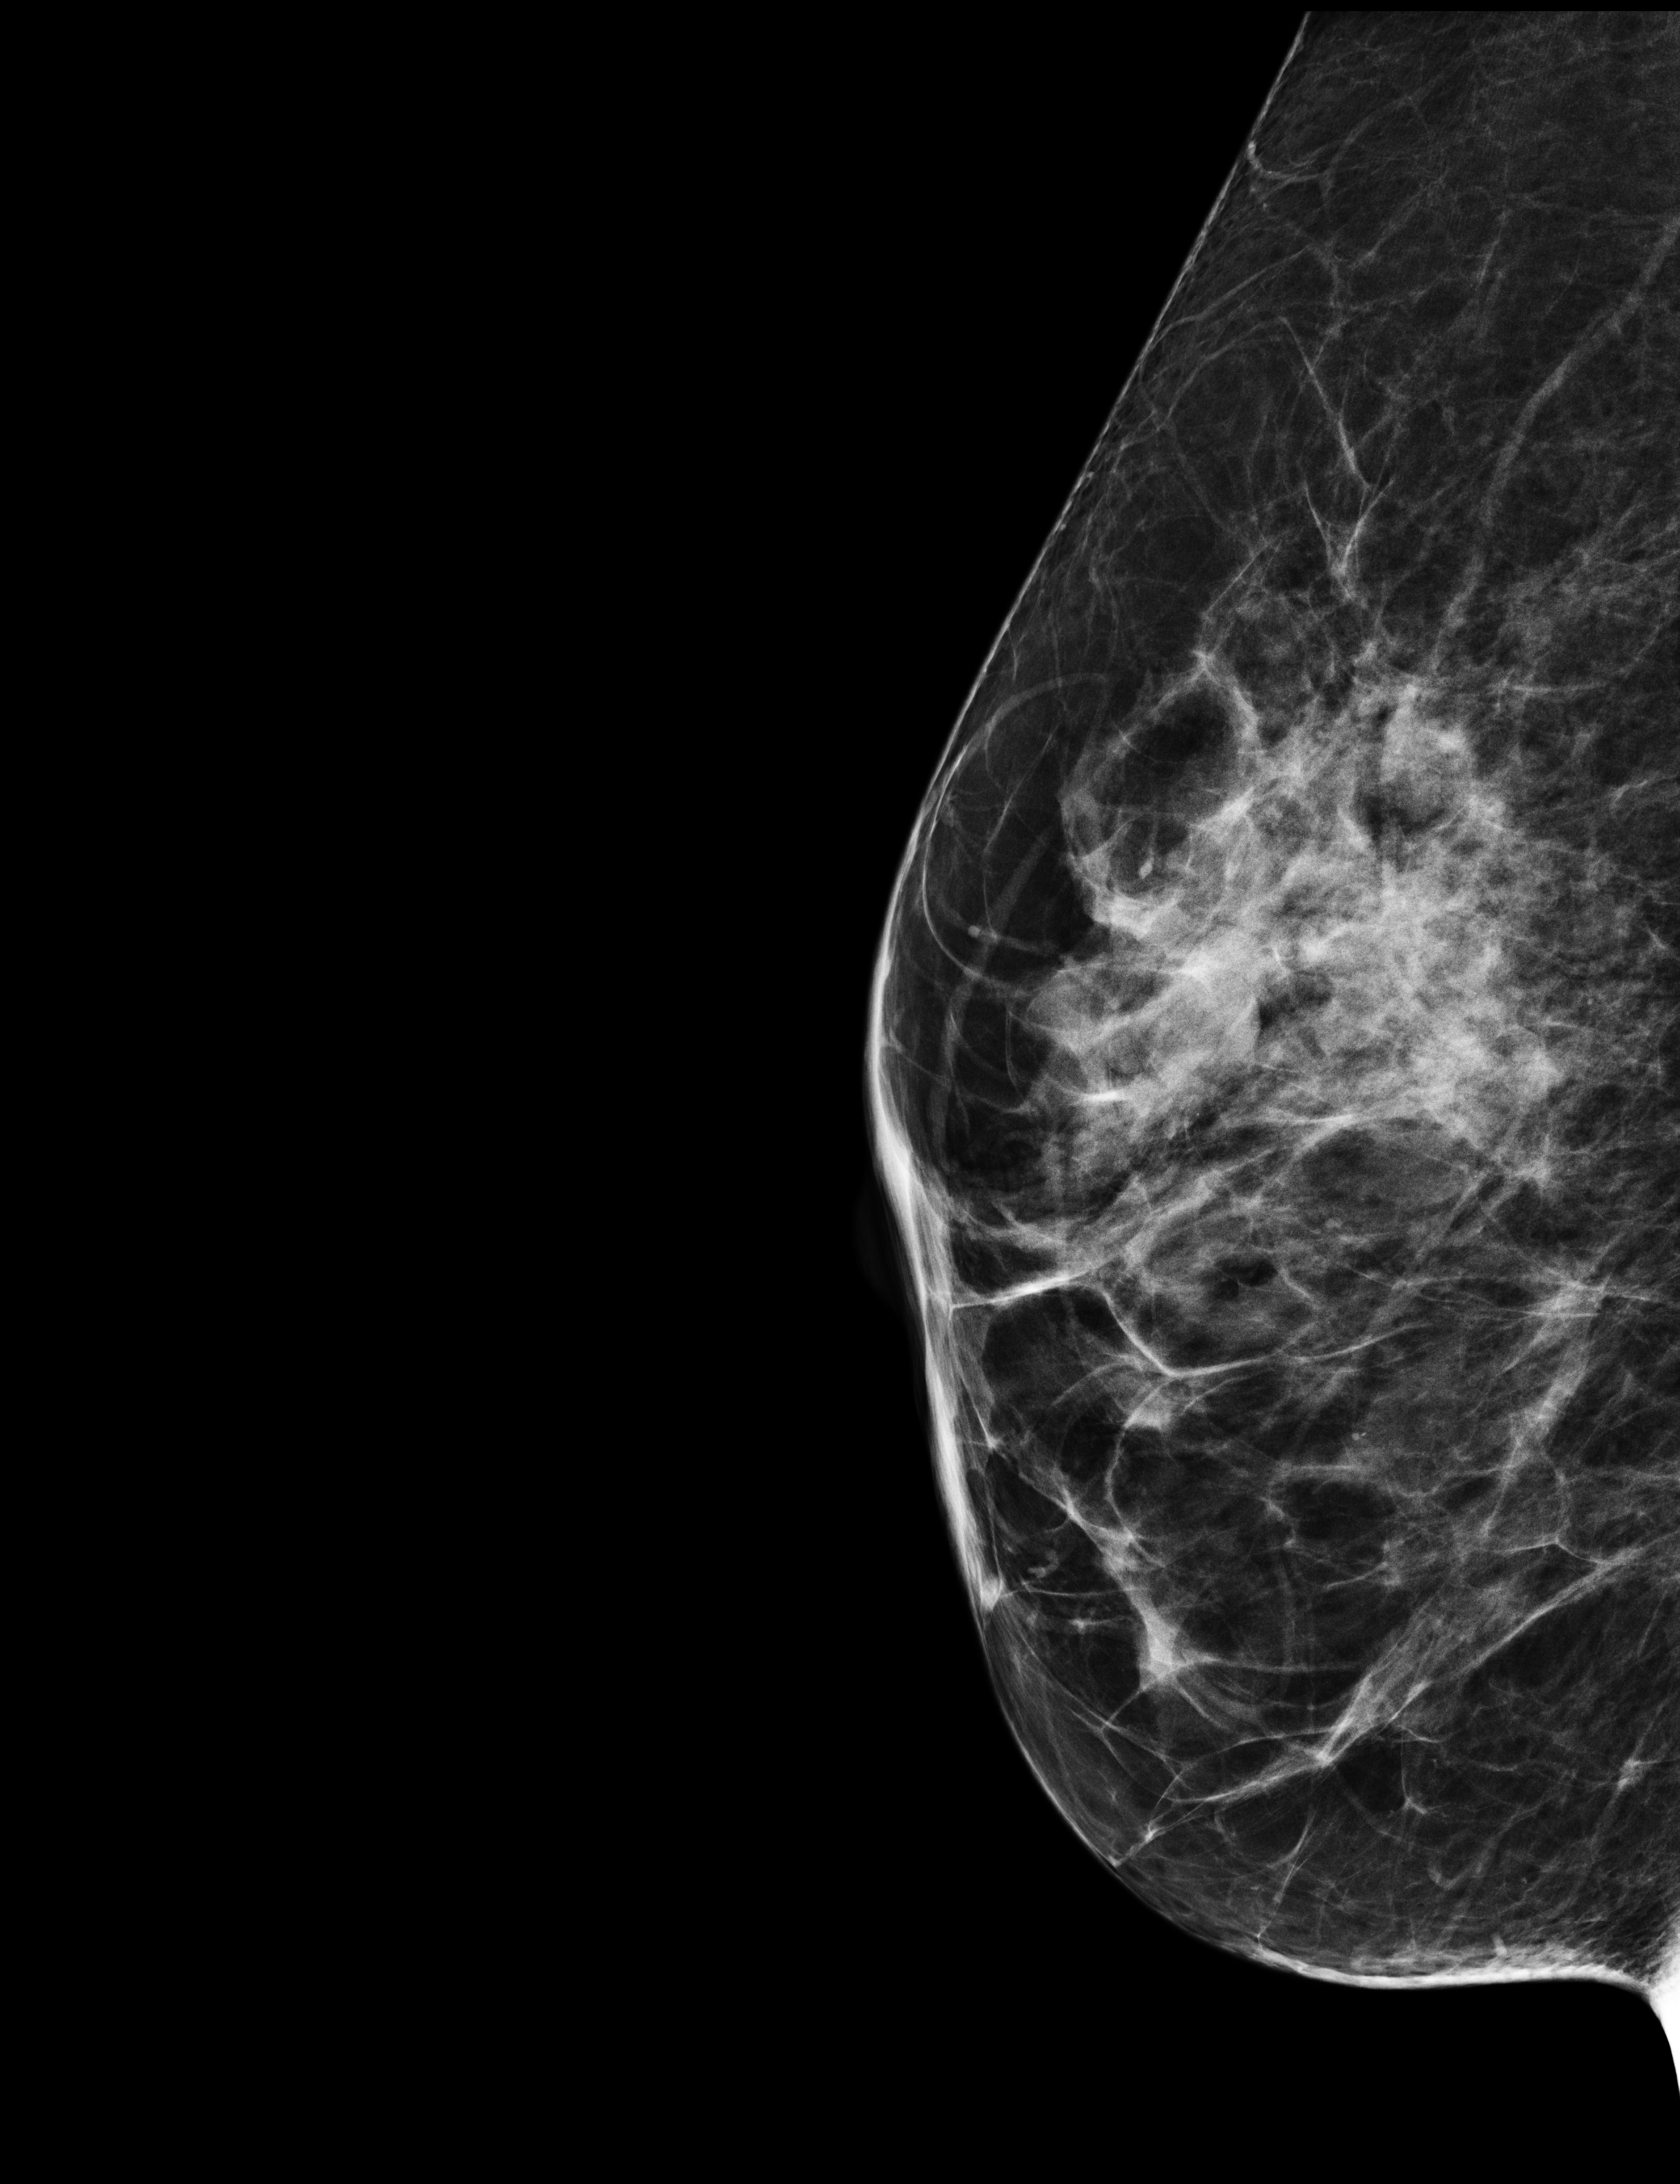
Diagnostic examination (additional views); compressed breast thickness 51 mm. Female patient, age 43 years.
Image type: full-field digital mammogram. Breast: right. Projection: mediolateral (ML) view.